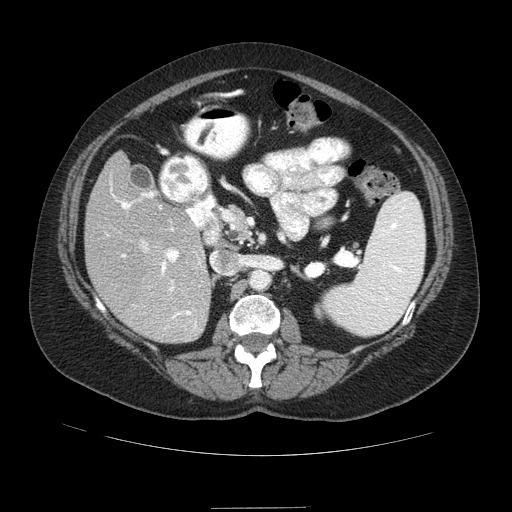
Contrast-enhanced abdominal CT (liver protocol), one axial slice; slice 39 of 89 in the series (ordered by position); reconstruction kernel STANDARD; 120 kVp; soft-tissue window (W 400 / L 40 HU); 512 × 512 image matrix. From the clinical record (not read from this slice): diagnosis: hepatocellular carcinoma (patient treated with transarterial chemoembolisation; whether this scan precedes or follows treatment is not stated here); TNM stage (as recorded): Stage-IIIB; Child-Pugh class: A.
Annotated regions visible in this slice (semi-automatic segmentation, software-assisted and operator-edited):
- liver parenchyma outside the tumour (the mass and vessels are separate outlines, so this box may not span the whole liver): box from (x=84, y=152) to (x=210, y=342) px
- liver vessels: (x=110, y=182)–(x=201, y=329)